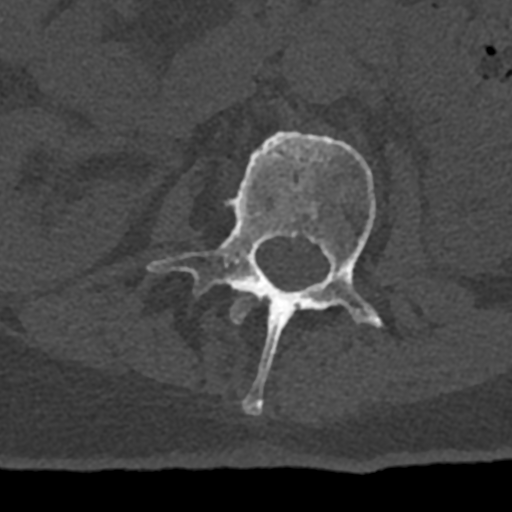
CT including the spine, one axial slice; position 381 of 797 along the scan axis; reconstruction kernel Br40s/3; bone window (W 1800 / L 400 HU); 0.5 mm slice thickness; 512 × 512 image matrix, field of view 160 × 160 mm. Patient: male, 74 years. Case-level facts recorded for this patient, not image findings: primary cancer: renal; vertebrae with lytic lesions (as recorded): T10, L1, L2, L3, L4, L5.
Outlined on this slice (semi-automatically segmented with operator editing):
- L1 vertebra: bounding box [x1, y1, x2, y2] px = [230, 291, 250, 323]
- L2 vertebra: [147, 131, 383, 415]